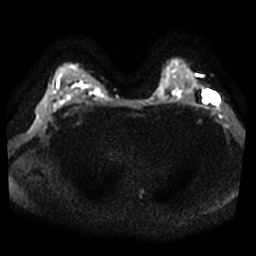
Breast MRI, one axial slice; position 30 of 38 along the scan axis; diffusion-weighted series; image 2 of 4 stored at this slice position (different b-values; order by instance number); 3 T; 5 mm slice thickness; 256 × 256 image matrix, field of view 360 × 360 mm. Female patient.
Annotated regions visible in this slice (manually delineated by an expert):
- tumour on diffusion-weighted imaging: bounding box <203,91,219,104> (left, top, right, bottom; pixels)